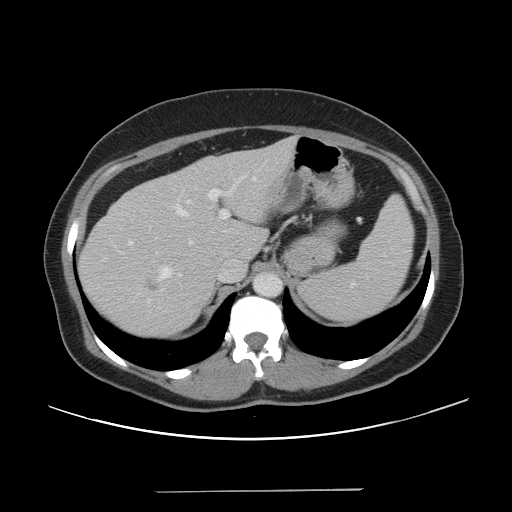
Contrast-enhanced abdominal CT, one axial slice; position 32 of 56 along the scan axis; intravenous contrast given; soft-tissue window (W 400 / L 40 HU); 512 × 512 image matrix, field of view 419 × 419 mm. Female patient, age 54 years. From the clinical record (not read from this slice): diagnosis: colorectal cancer liver metastases, imaged before liver resection; multiple liver metastases: yes; largest metastasis: 3.2 cm.
Structures marked on this image (outlined manually by an expert reader):
- hepatic veins: bounding box (x1, y1, x2, y2) in pixels: (161, 178, 256, 278)
- liver: (79, 137, 298, 339)
- planned liver remnant (the part of the liver to remain after resection): (180, 137, 298, 262)
- portal vein (with intrahepatic branches): (207, 178, 244, 220)
- liver metastasis: (148, 277, 159, 291)